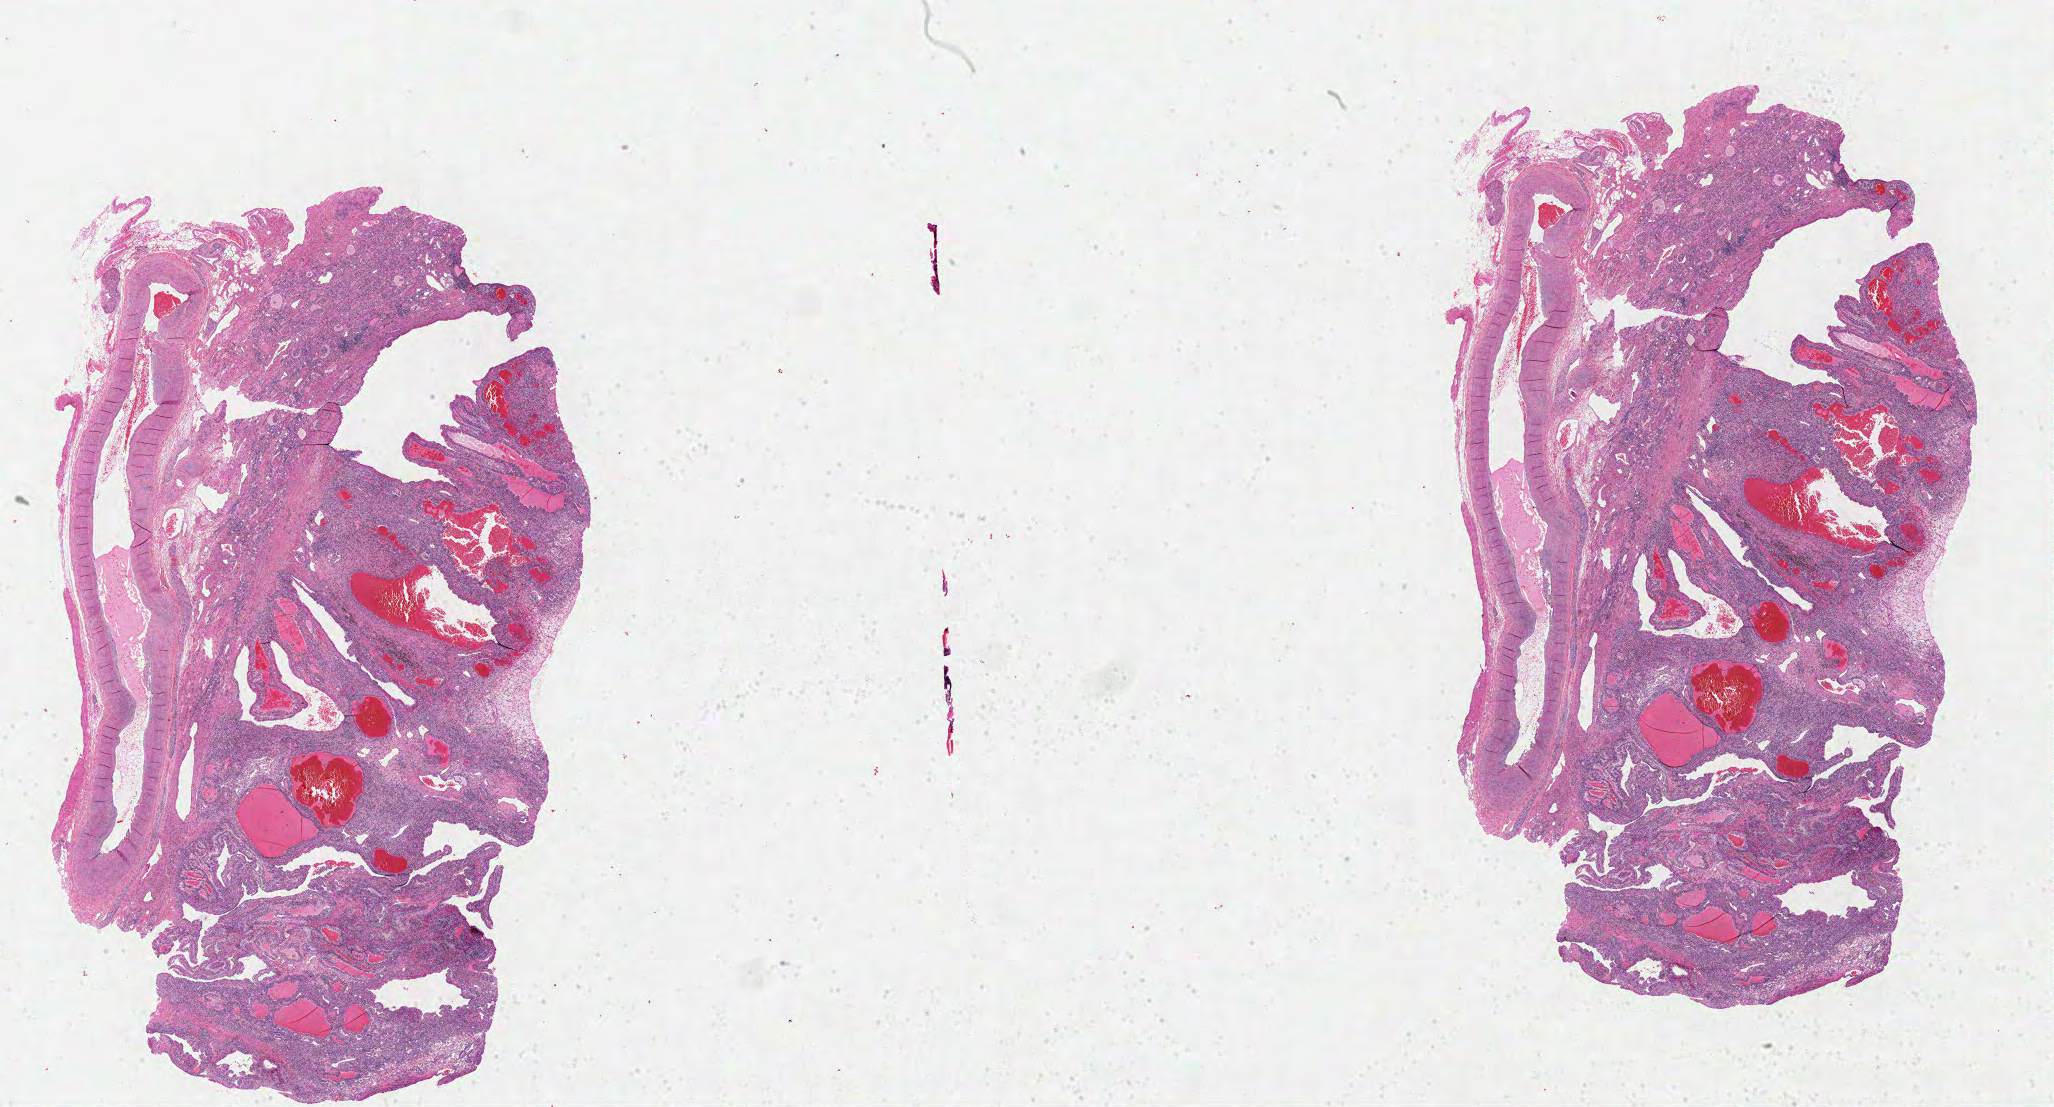
Digitized H&E tissue section (whole slide), whole scanned area (about 32.3 x 17.4 mm) shown as a low-resolution overview. Formalin-fixed paraffin-embedded (FFPE) diagnostic section. Sample: primary tumour, kidney. Patient: male, age at initial diagnosis 42 years. Histologic grade: G2 (moderately differentiated).
TNM: T1a N0 M0. AJCC pathologic stage: I. Diagnosis: Clear cell adenocarcinoma, NOS.